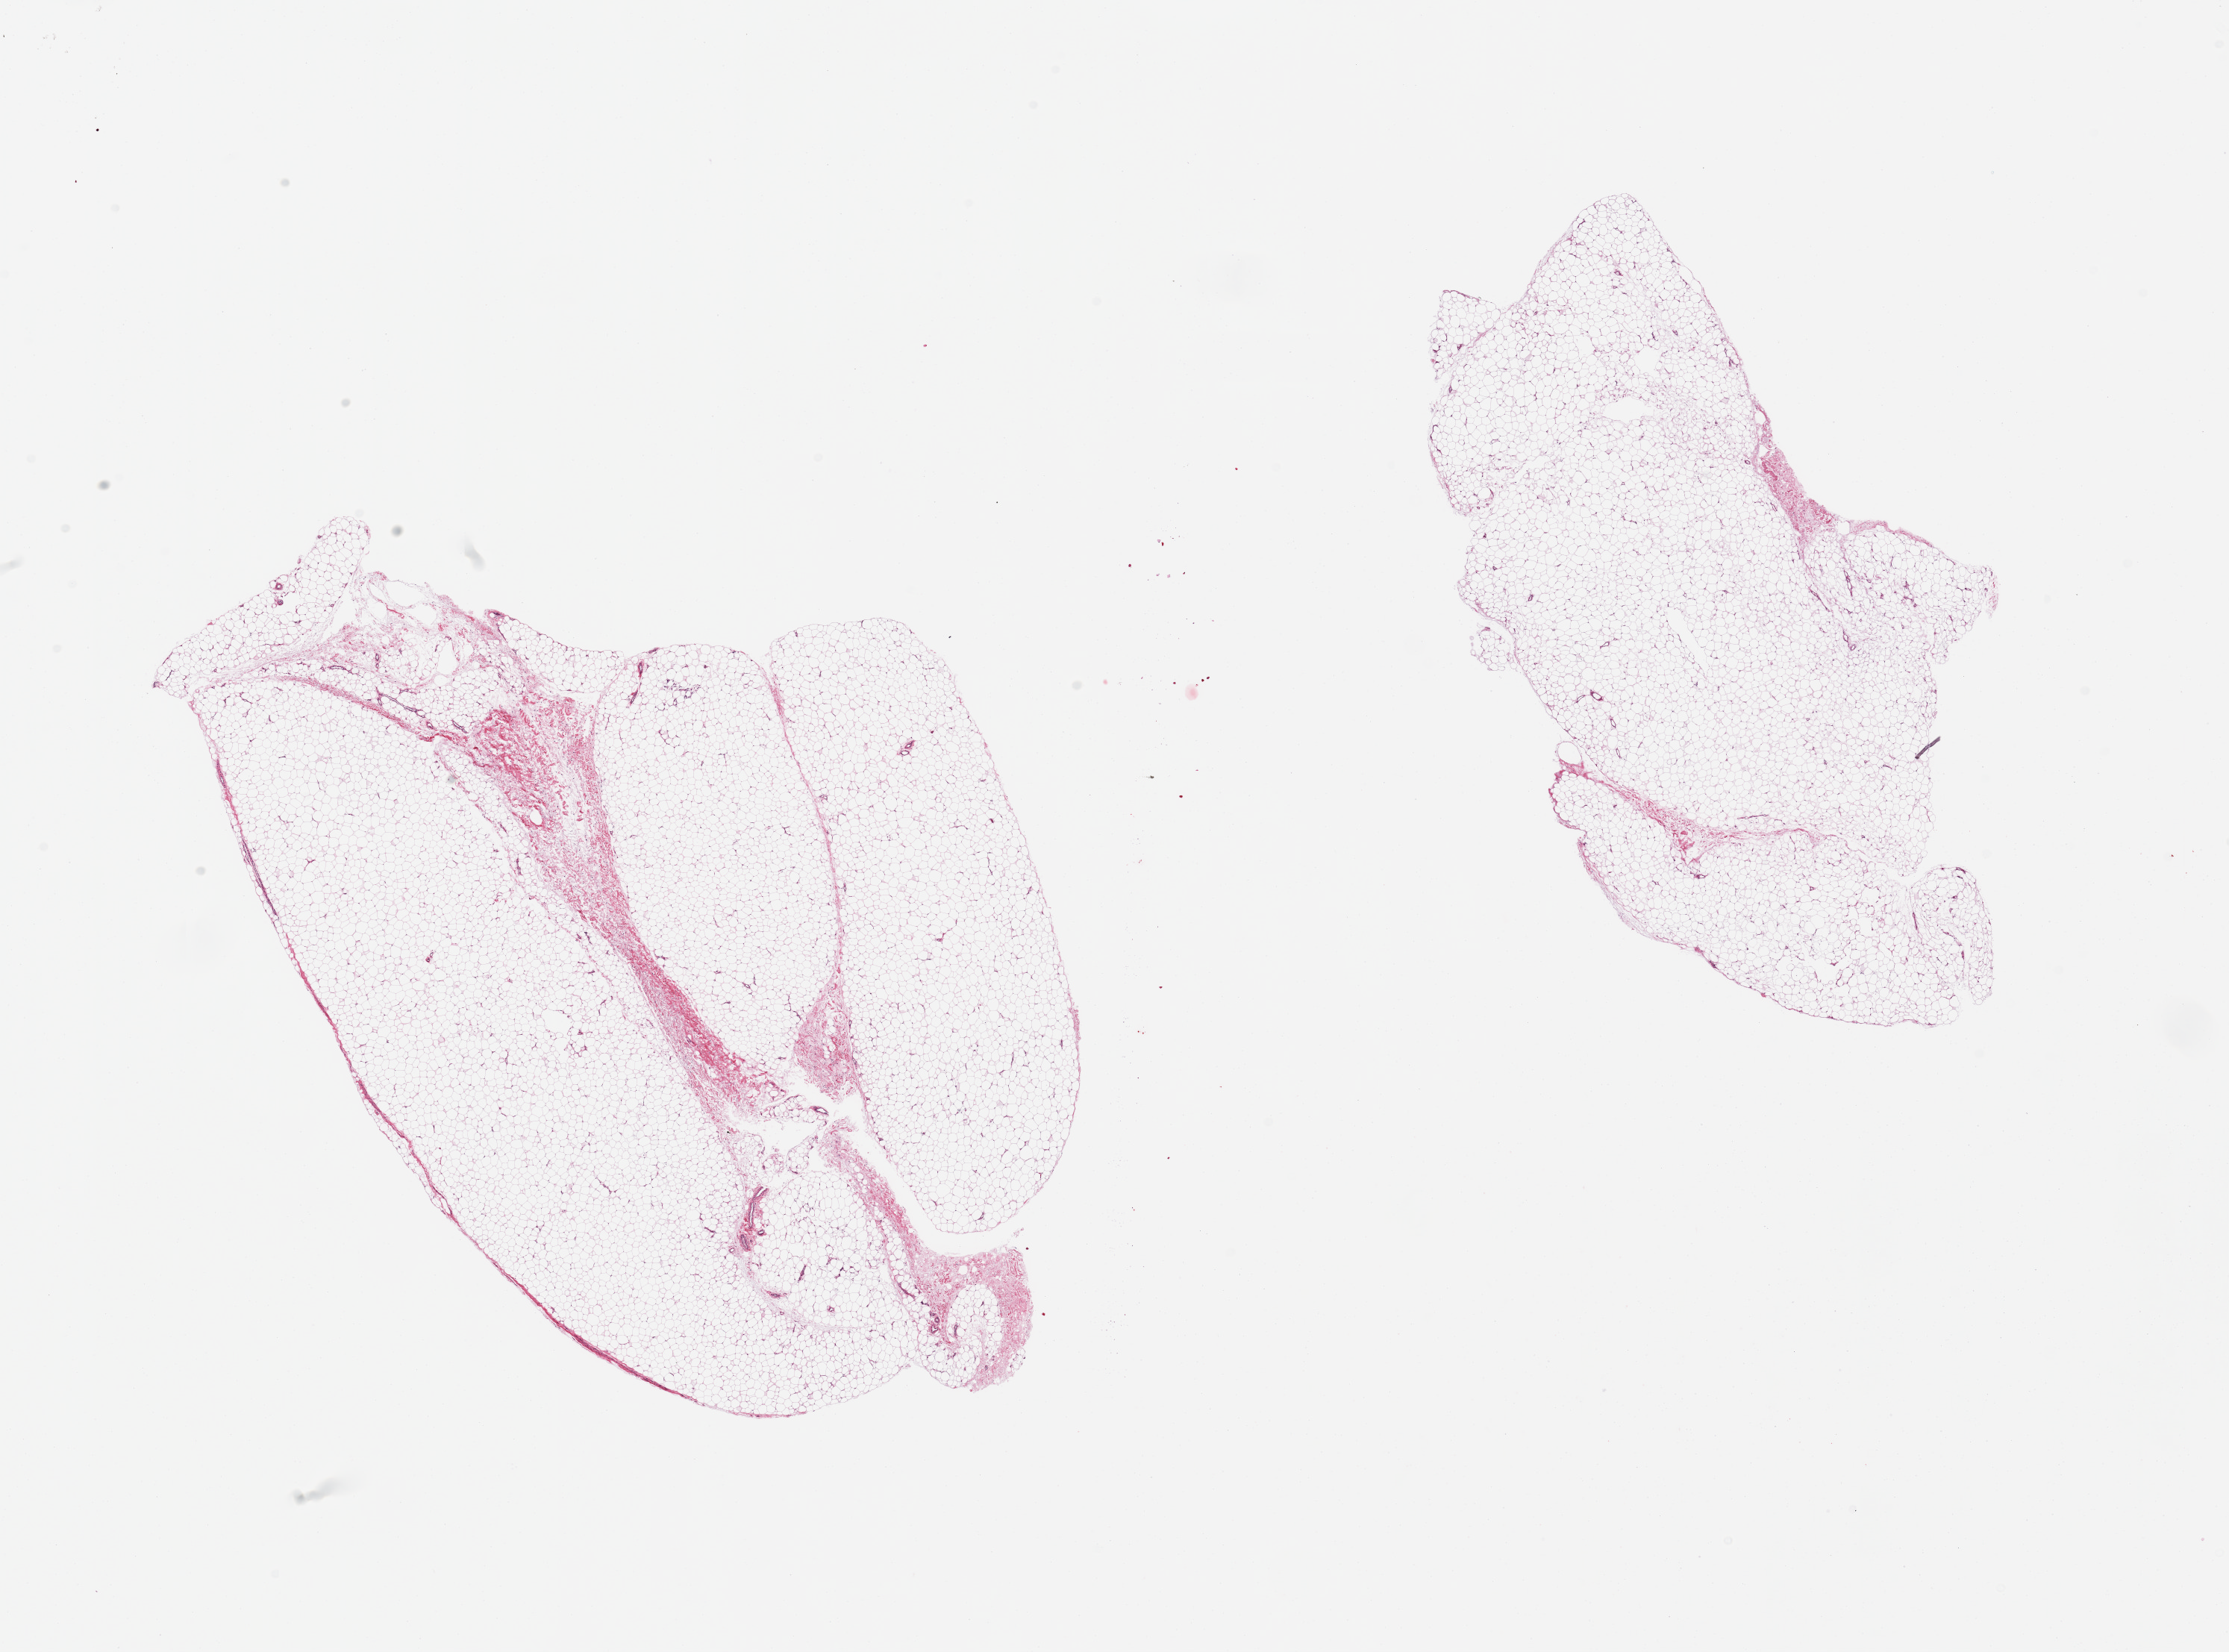
Whole-slide image, haematoxylin and eosin stain, a low-resolution overview of the entire scanned area, about 23.6 x 17.5 mm (acquisition: 20x scan), PAXgene-fixed, paraffin-embedded tissue, section of adipose tissue (target tissue), tissue donor sample. Donor: male.
Reviewer comment on this tissue sample: 2 pieces; ~10% fascia/vascular elements.